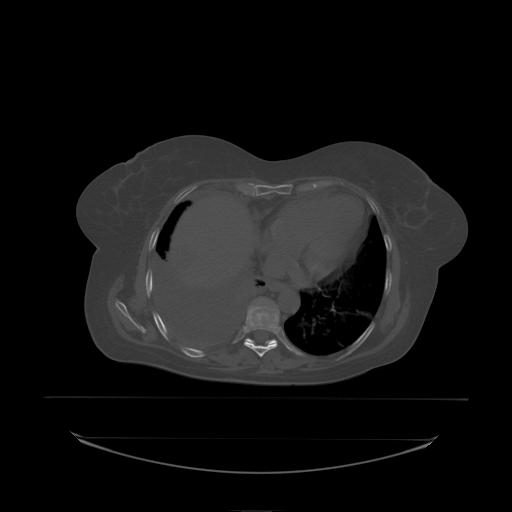
CT including the spine, one axial slice; position 130 of 242 along the scan axis; bone window (W 1800 / L 400 HU); 2.5 mm slice thickness; 512 × 512 image matrix, field of view 500 × 500 mm. Female patient, age 53 years. Case-level facts recorded for this patient, not image findings: primary cancer: lung.
Outlined on this slice (semi-automatically segmented with operator editing):
- T8 vertebra: bounding box <246,299,280,334> (left, top, right, bottom; pixels)
- T9 vertebra: <263,299,265,301>